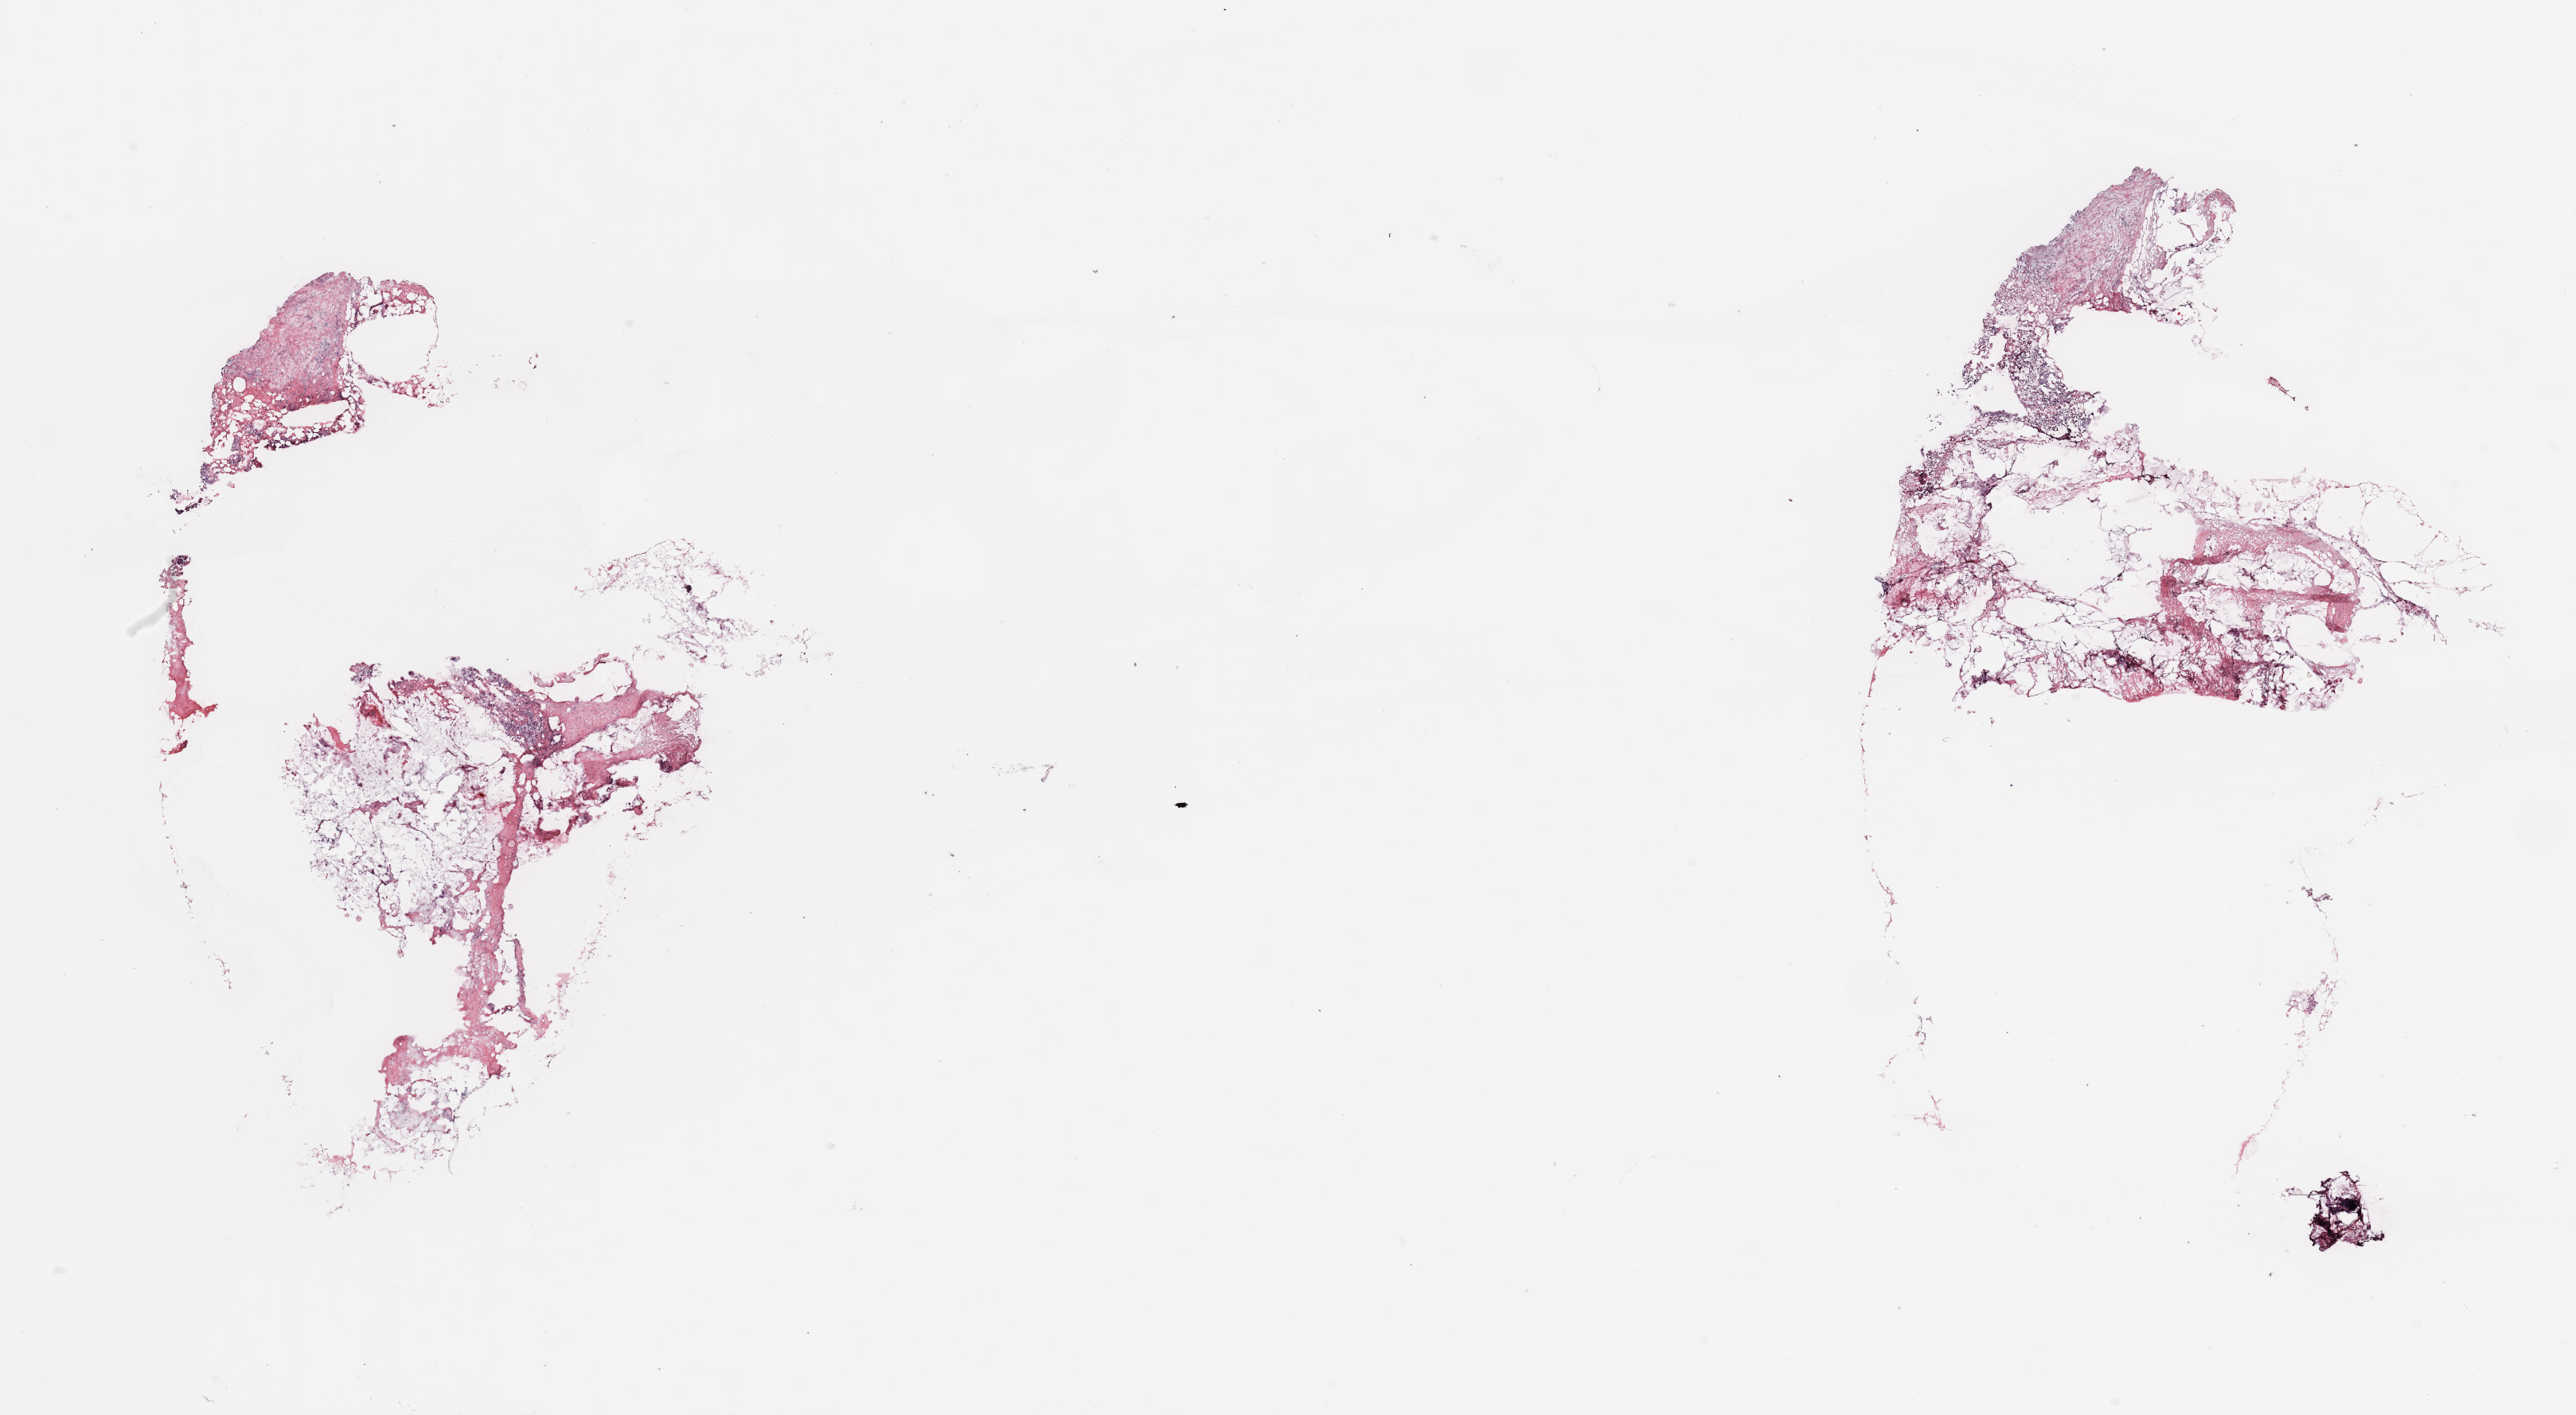
H&E whole-slide image — whole scanned area (about 25.6 x 14.1 mm, slide scanned at 20x) shown as a low-resolution overview, breast, tissue type not recorded.
Patient diagnosis (cohort enrolment): breast cancer (breast).